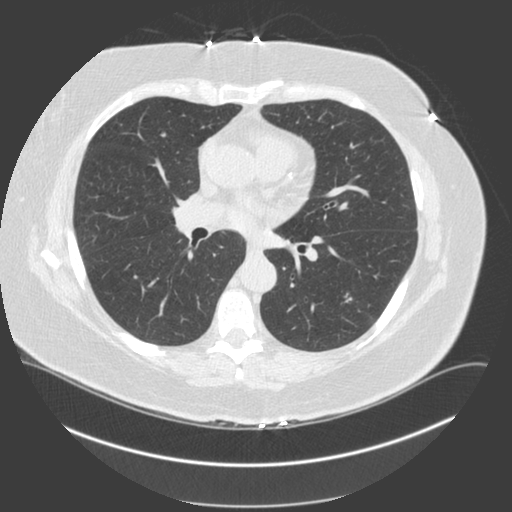
Chest CT (low-dose screening protocol), one axial image; second screening round (one year after baseline); lung window (W 1500 / L -600 HU); slice 76 of 179 in the series. Female, age 66 years at enrolment. Current smoker at enrolment.
- Lesion marked by an expert reader, bounding box [x1, y1, x2, y2] px = [329, 283, 365, 317].
- No non-calcified nodule or mass ≥4 mm was recorded by the screening reader at this exam.
- Official screen result: negative screen, minor abnormalities not suspicious for lung cancer.
- Later outcome: lung cancer diagnosed 495 days after this screen — non-small cell carcinoma, left lower lobe, poorly differentiated (G3), stage IA (AJCC 6th edition), 20 mm at pathology.